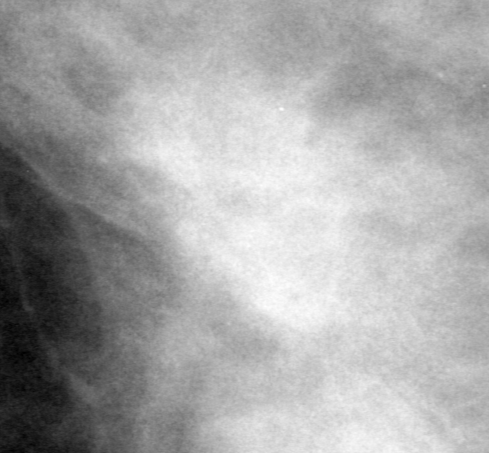
Region of interest cut from a scanned film mammogram (one marked finding); right breast; CC view; BI-RADS breast density category 4 (scale 1–4).
- Finding: mass, shape architectural distortion, margins spiculated; BI-RADS assessment category 4; subtlety rating 2 on a 1 (subtle) to 5 (obvious) scale; pathology result (as recorded, not read from the image): malignant.